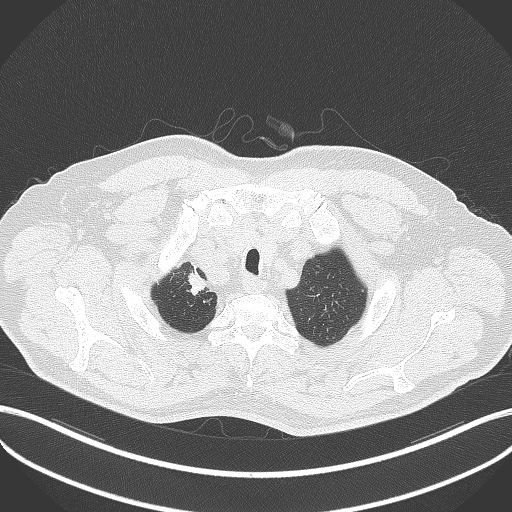
Chest CT, one axial slice; slice 347 of 411 in the series (ordered by position); reconstruction kernel B70f; 120 kVp; lung window (W 1500 / L -600 HU); 1 mm slice thickness; 512 × 512 image matrix, field of view 400 × 400 mm. Patient: male, 60 years. Case-level facts recorded for this patient, not image findings: clinical TNM (as recorded): T1b N1 M0.
Structures marked on this image (bounding box drawn by a radiologist):
- lung tumour (recorded histology: squamous cell carcinoma): bounding box [x1, y1, x2, y2] px = [184, 268, 208, 298]